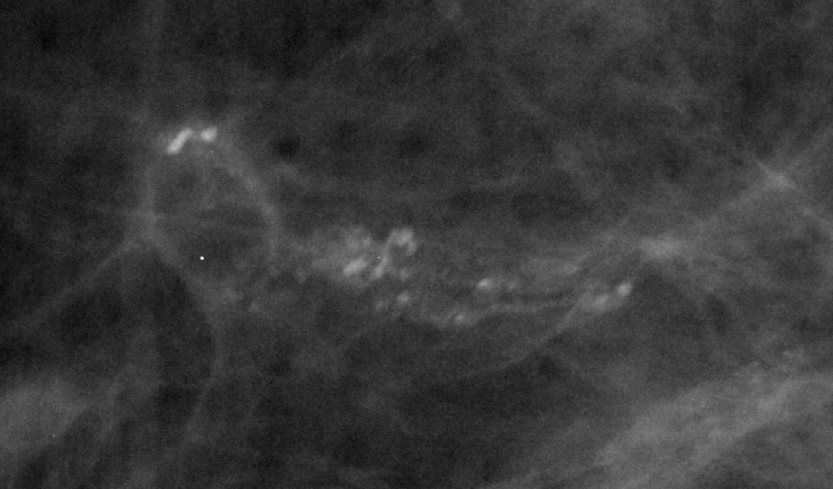
Crop from a digitized film mammogram around one marked abnormality; right breast; MLO view; BI-RADS breast density category 1 (scale 1–4).
- Finding: calcifications, morphology pleomorphic, distribution segmental; BI-RADS assessment category 4; pathology (as recorded): benign.